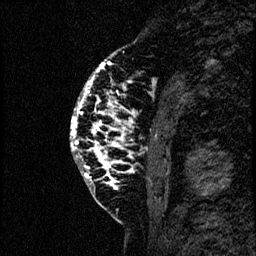
Breast MRI (dynamic contrast-enhanced), one sagittal slice; slice 20 of 60 in the series (ordered by position); dynamic contrast-enhanced study with each time point stored as its own series, time point 2 of 4 at this slice position (early post-contrast, ordered by acquisition time); 1.5 T; TE 4.2 ms, TR 17.6 ms; 256 × 256 image matrix, field of view 200 × 200 mm. Female patient, age 40 years. Case-level facts recorded for this patient, not image findings: setting: breast cancer imaged before/during neoadjuvant chemotherapy; receptor status: HER2-positive.
Outlined on this slice (semi-automatic segmentation, software-assisted and operator-edited):
- analysis volume of interest (the breast-tissue region the enhancement analysis was run in; not a lesion): bounding box [x1, y1, x2, y2] px = [66, 55, 184, 206]
- tumour enhancement mask (voxels above the 100 % enhancement threshold inside the analysis volume of interest): [70, 62, 132, 185]